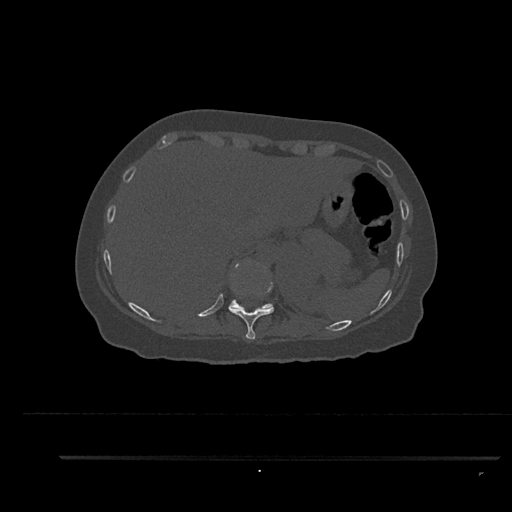
CT including the spine, one axial slice. Slice 347 of 797 in the series (ordered by position). Reconstruction kernel Br40s/3. 120 kVp. Bone window (W 1800 / L 400 HU). 512 × 512 image matrix, field of view 408 × 408 mm. Patient: female, 44 years. From the clinical record (not read from this slice): primary cancer: renal; vertebrae with lytic lesions (as recorded): L1.
Structures marked on this image (semi-automatically segmented with operator editing):
- T10 vertebra: bounding box (x1, y1, x2, y2) in pixels: (228, 261, 274, 340)
- T11 vertebra: (229, 263, 274, 310)